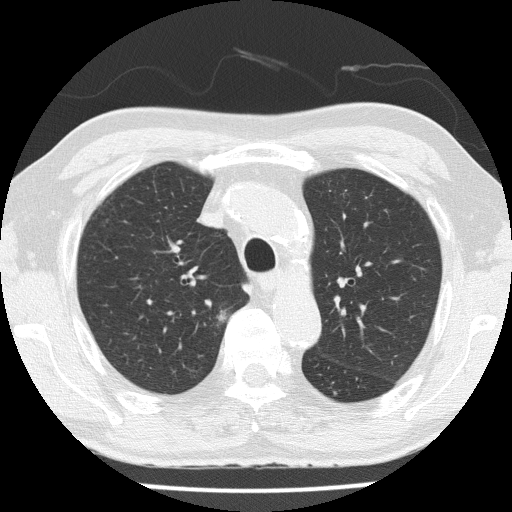
Low-dose screening chest CT, one axial slice. Position 108 of 153 along the scan axis. 120 kVp. Lung window (W 1500 / L -600 HU). 512 × 512 image matrix.
Structures marked on this image (outlined manually by an expert reader):
- lesion 1 (tumor, upper lobe of right lung): box from (x=220, y=311) to (x=231, y=326) px